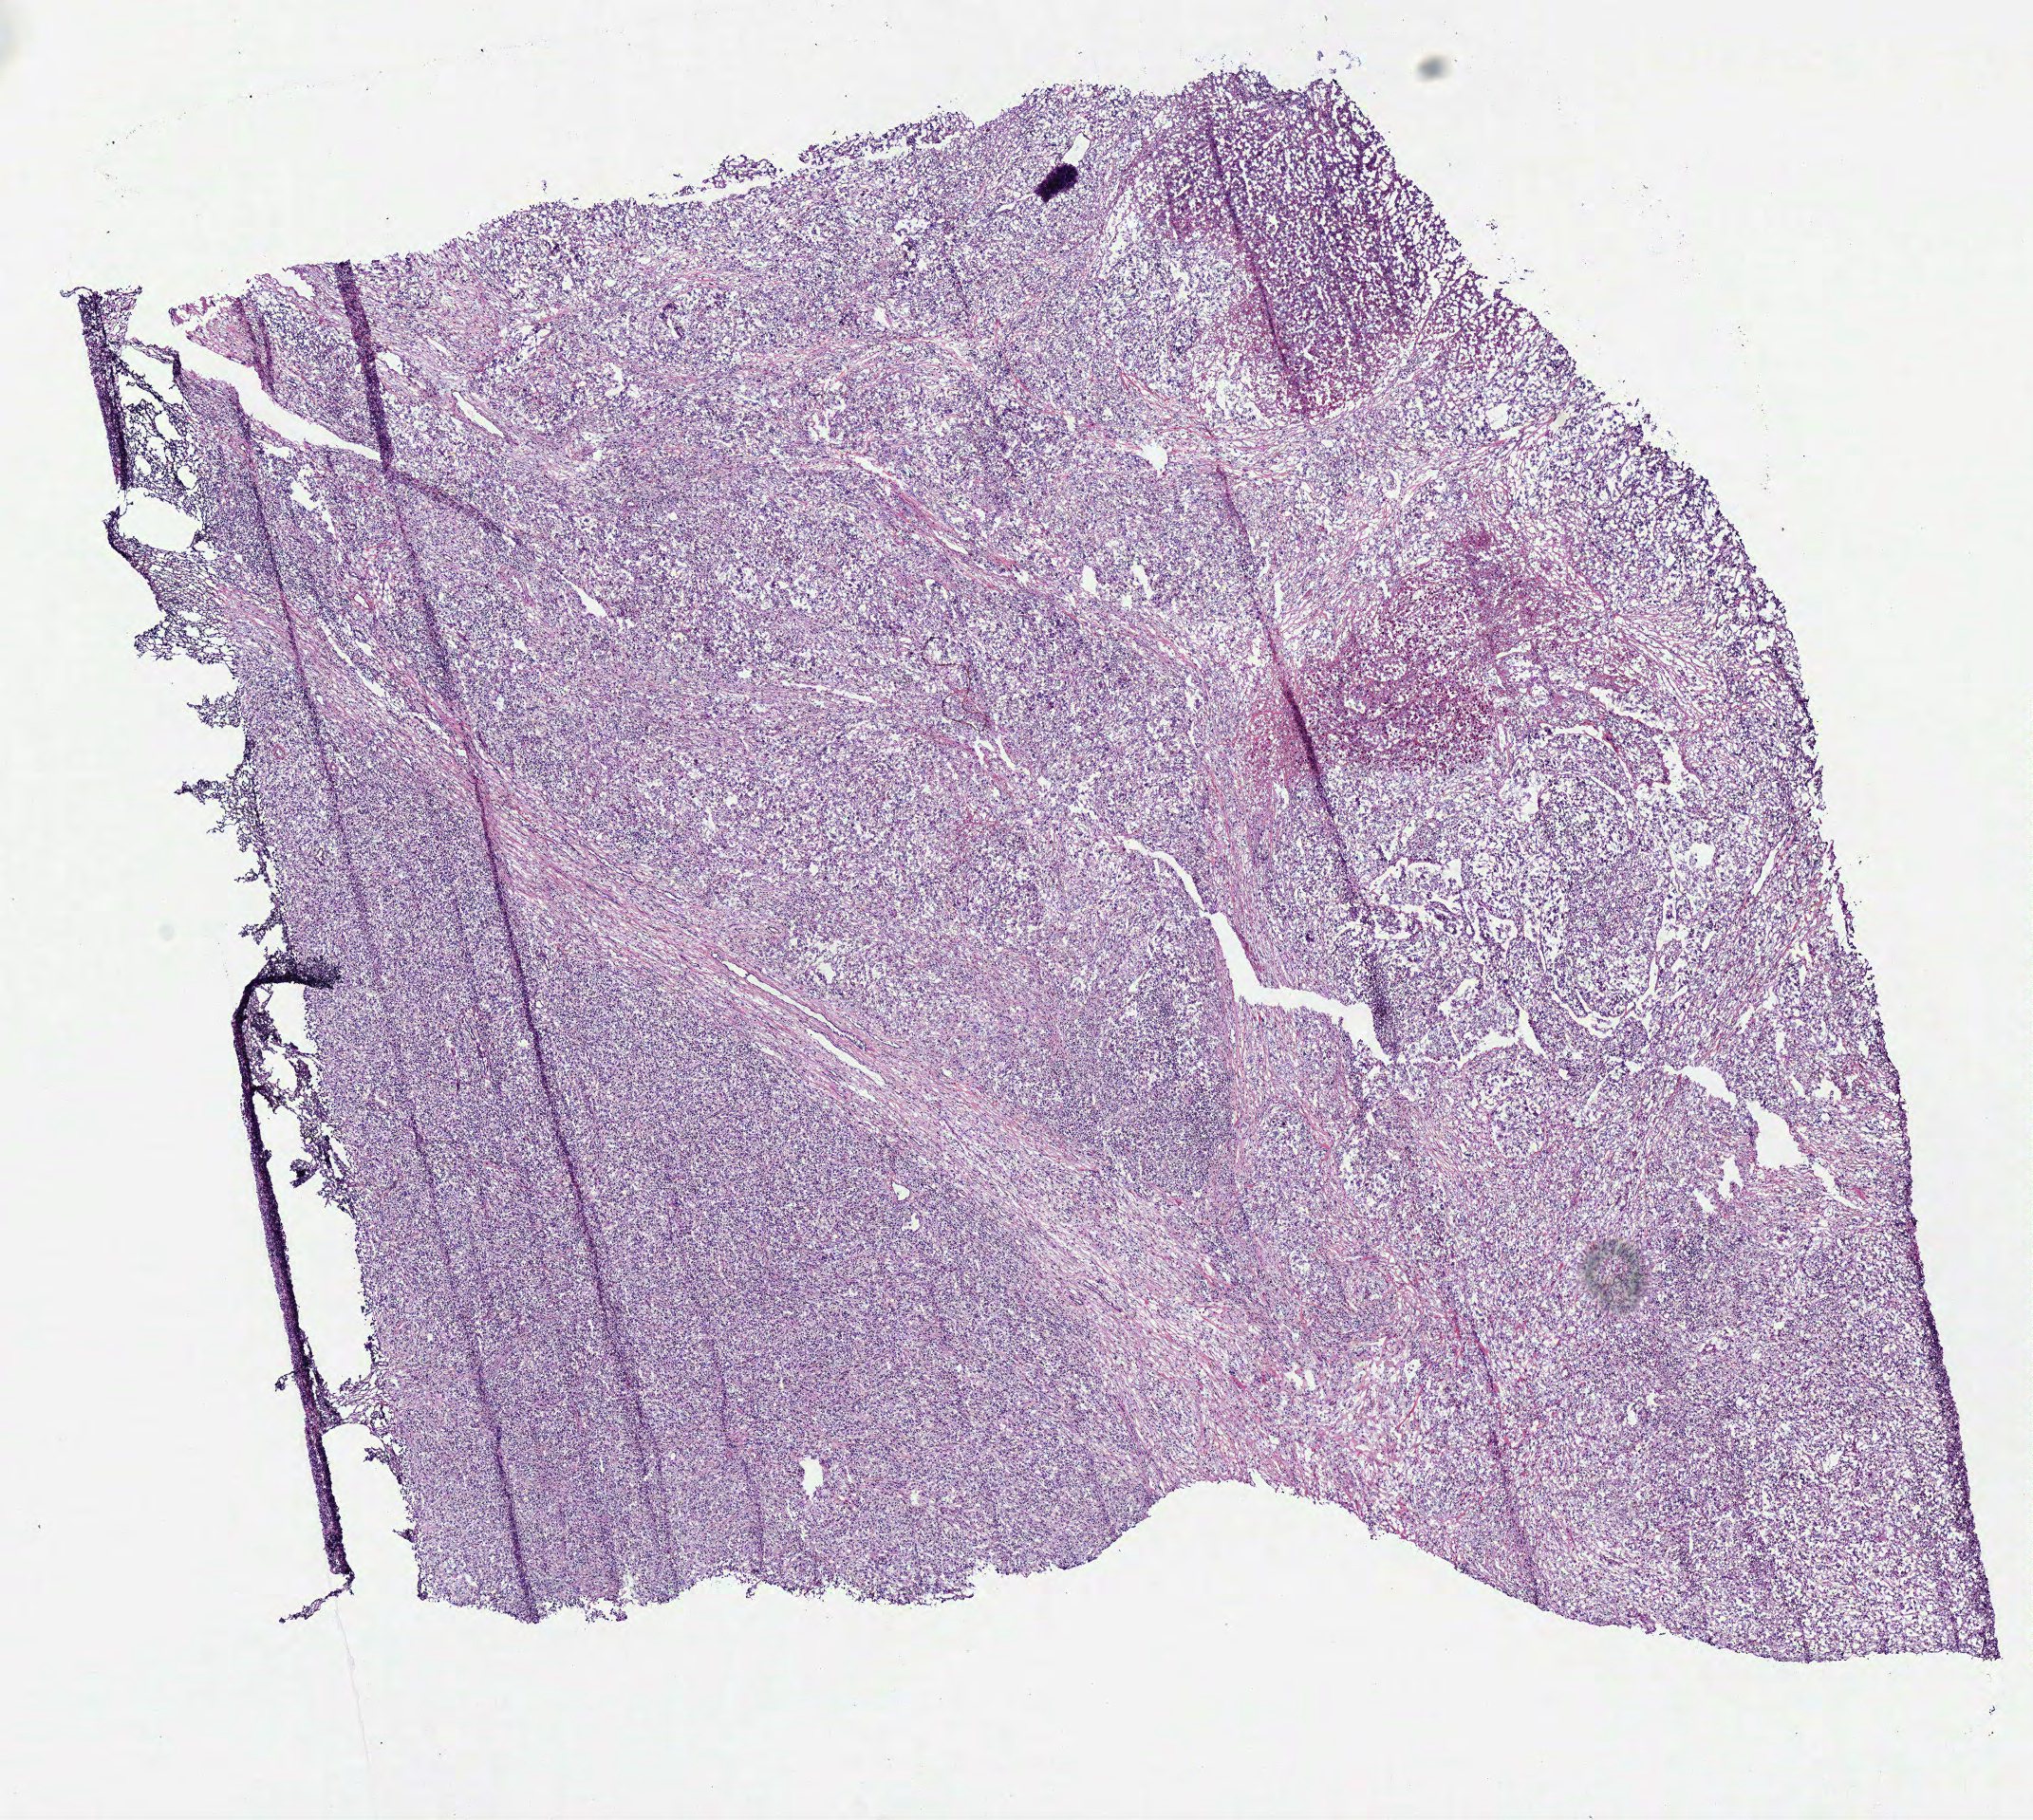
Whole-slide histology image, H&E — whole scanned area (about 8.4 x 7.6 mm, from a 40x scan) shown as a low-resolution overview; frozen section; kidney, primary tumour sample. Patient: male, age at initial diagnosis 61 years. Histologic grade: G4 (undifferentiated). Composition of this section per pathologist review: tumour cells 80%, tumour nuclei 85%, normal cells 0%, stromal cells 12%, necrosis 8%.
Diagnosis: Clear cell adenocarcinoma, NOS. AJCC pathologic stage: IV. Laterality: right.